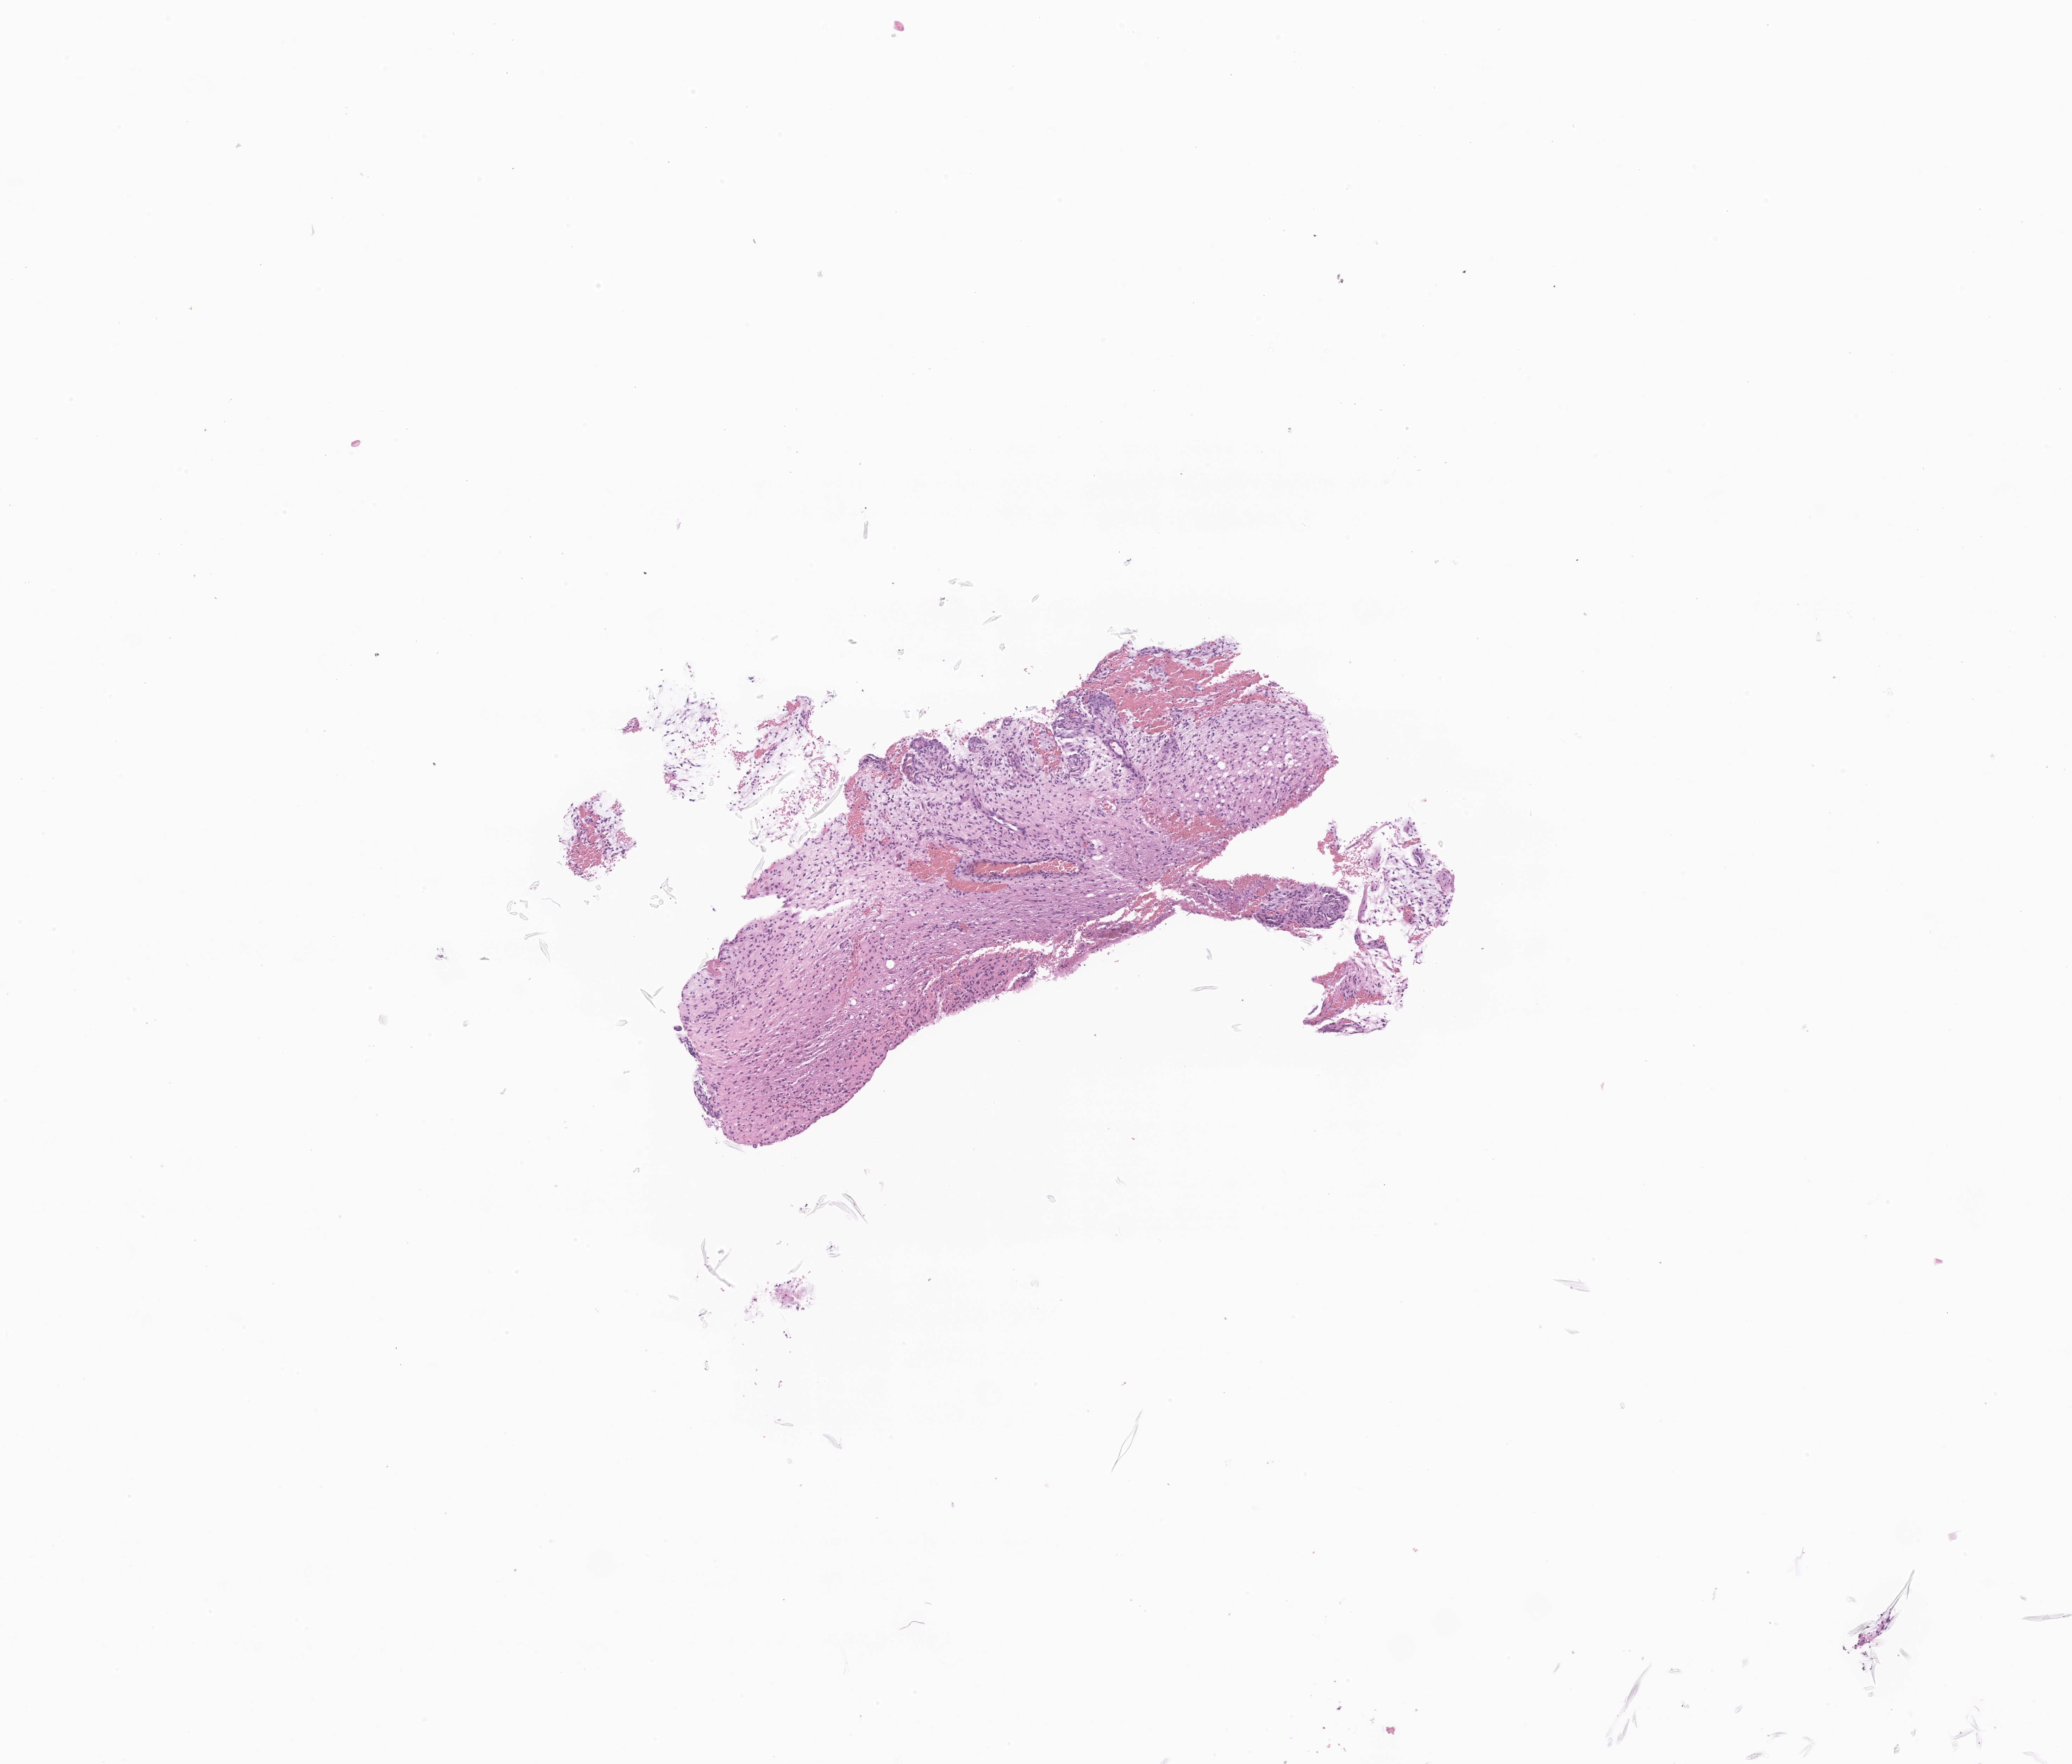
Digitized hematoxylin and eosin (H&E)-stained section of tumor tissue from the brain, whole scanned area (about 6.2 x 5.3 mm) shown as a low-resolution overview. Formalin-fixed, paraffin-embedded (FFPE) tissue. Patient: female, age 854 days (about 2.3 years).
Recorded diagnosis: Pilocytic astrocytoma.